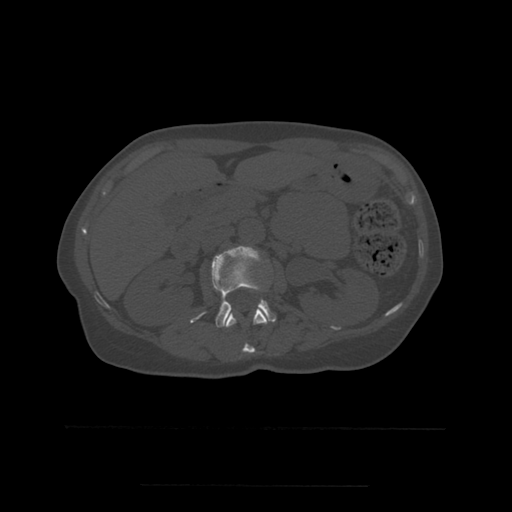
CT including the spine, one axial slice. Slice 222 of 544 in the series (ordered by position). Bone window (W 1800 / L 400 HU). 1.25 mm slice thickness. 512 × 512 image matrix. Patient age 58 years. From the clinical record (not read from this slice): primary cancer: lung.
Structures marked on this image (semi-automatic segmentation, software-assisted and operator-edited):
- L1 vertebra: box from (x=226, y=309) to (x=268, y=354) px
- L2 vertebra: (x=190, y=246)–(x=277, y=328)